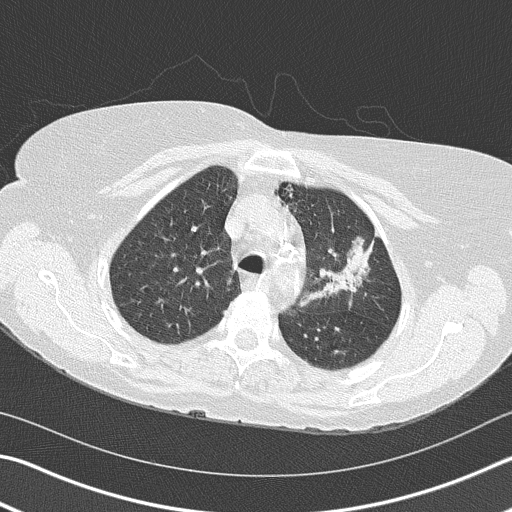
Chest CT (low-dose screening protocol), one axial image; second annual screen; lung window (W 1500 / L -600 HU); 2 mm slice thickness; lung (sharp) reconstruction kernel (B50f); slice 121 of 153 in the series; 512 × 512 image matrix, field of view 342 × 342 mm. Female participant, aged 68 years at enrolment. Former smoker at enrolment.
Expert-annotated lung lesion, box from (x=292, y=214) to (x=384, y=317) px. Reader record for this screening exam (exam-level; its link to the box is not recorded): non-calcified nodule or mass ≥4 mm, left upper lobe, 4 × 2 mm, spiculated (stellate) margins, soft tissue attenuation, pre-existing on the prior screen: yes; interval growth: yes. Official screen result: positive, other. Later outcome: lung cancer diagnosed 392 days after this screen (after the third annual screen) — adenocarcinoma, NOS, left upper lobe, poorly differentiated (G3), stage IB (AJCC 6th edition), 50 mm at pathology.